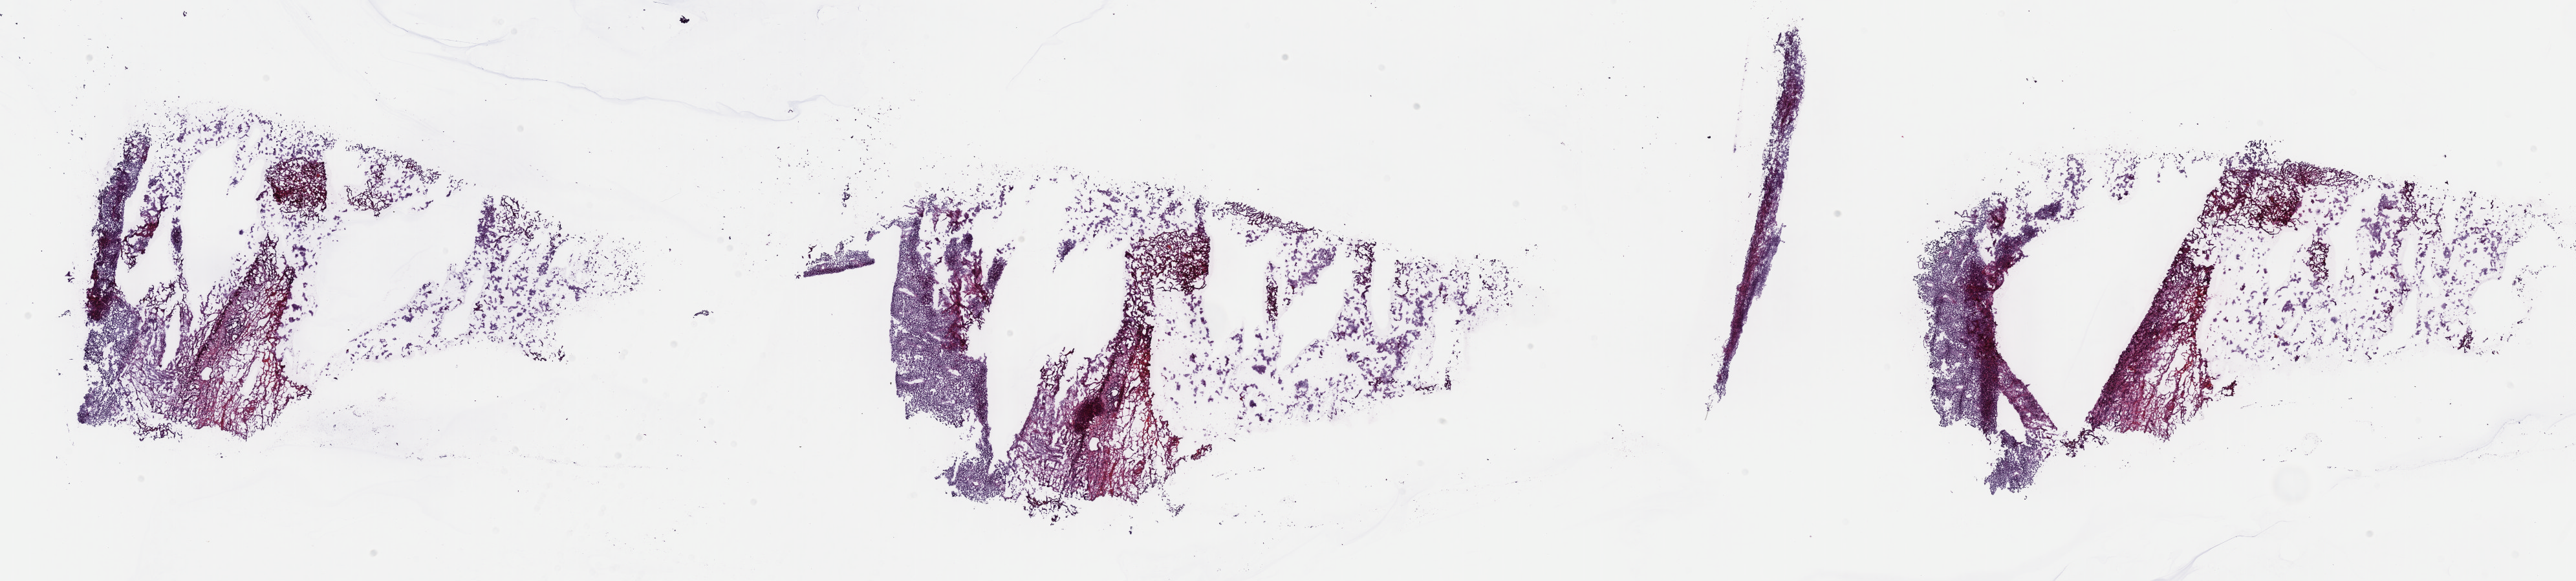
H&E whole-slide image, low-resolution overview of the scanned area, about 32.2 x 7.3 mm (slide scanned at 40x), frozen section from the top of the tissue portion, bladder, primary tumour sample. Female patient; age at initial diagnosis 64 years. Histologic grade: high grade. Composition of this section per pathologist review: tumour cells 100%, tumour nuclei 60%, normal cells 0%, stromal cells 0%, necrosis 0%. Infiltration values recorded for this section: lymphocyte infiltration 2%, monocyte infiltration 0%, neutrophil infiltration 0%.
AJCC pathologic stage: II (7th edition). Histologic diagnosis: Transitional cell carcinoma (anterior wall of bladder). TNM: N0 M0.